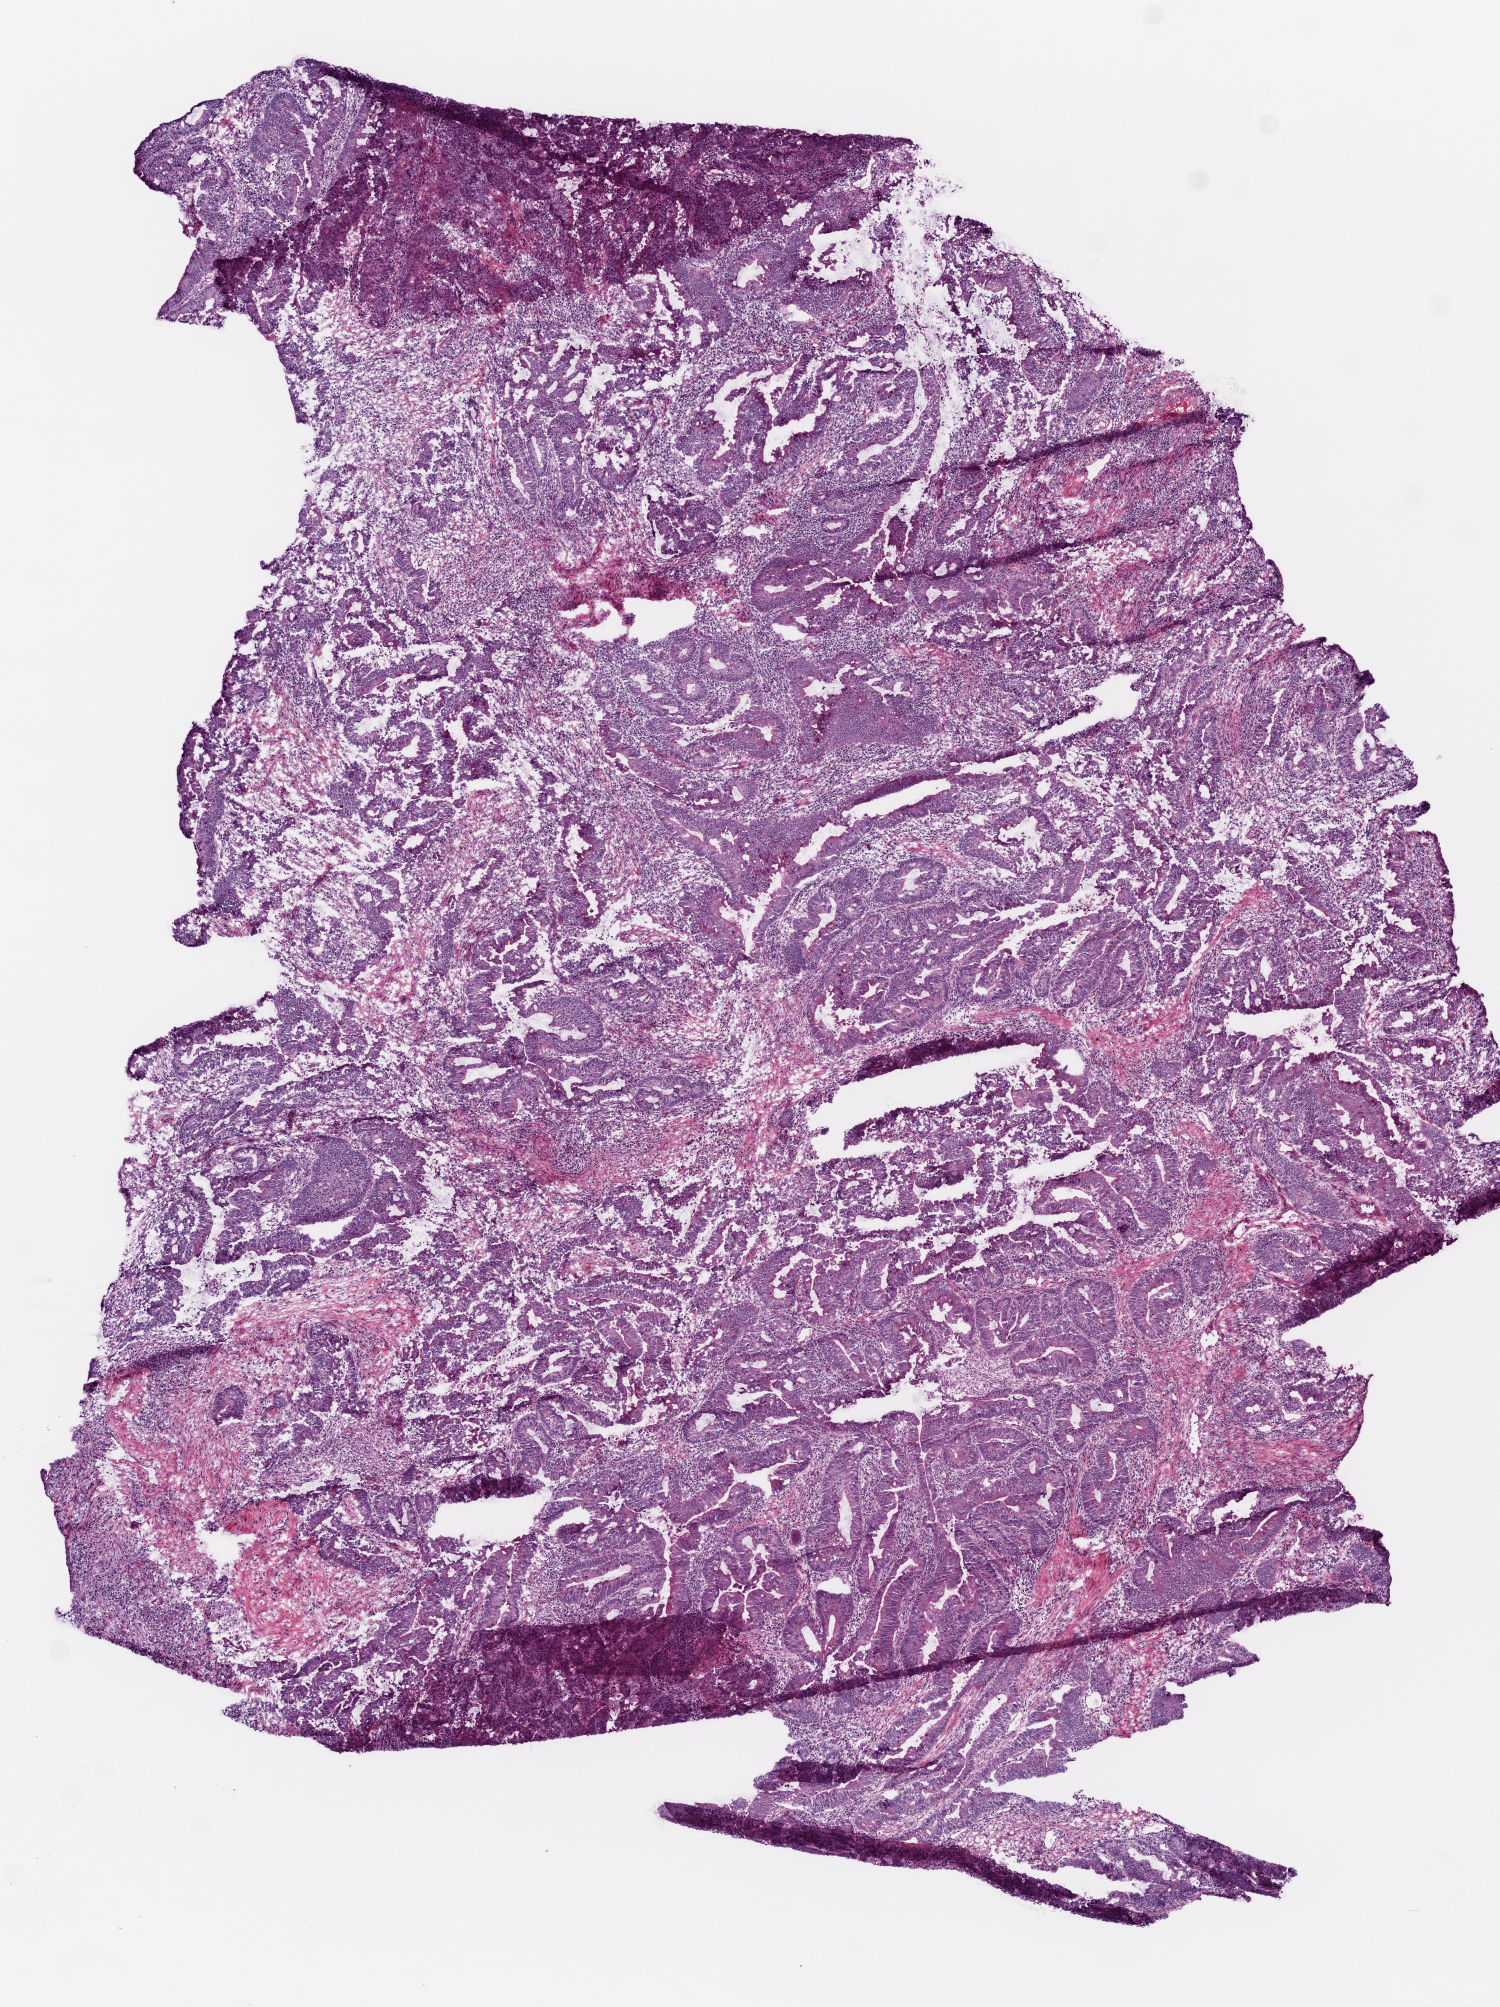
Whole-slide histology image, H&E-stained, whole scanned area (about 6.0 x 8.1 mm) shown as a low-resolution overview; frozen section from the top of the tissue portion; sample: primary tumour, colon. Male, age 84 years at initial diagnosis. Composition of this section per pathologist review: tumour cells 80%, tumour nuclei 88%, normal cells 10%, stromal cells 8%, necrosis 2%.
AJCC pathologic stage: IV. Lymph nodes positive (case pathology): 5 of 19 examined. Diagnosis: Adenocarcinoma, NOS.